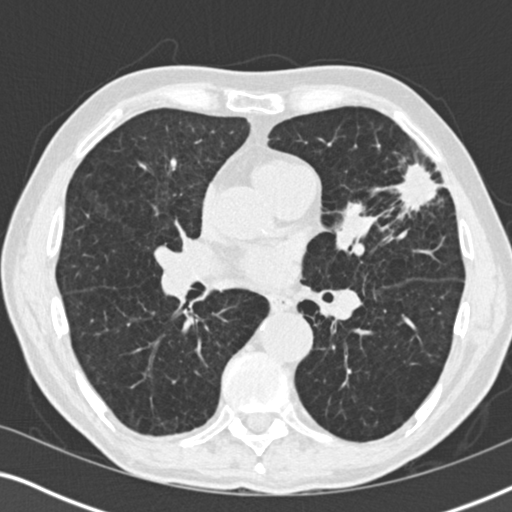
Low-dose screening chest CT, one axial slice; position 99 of 196 along the scan axis; 120 kVp; lung window (W 1500 / L -600 HU); 2 mm slice thickness; 512 × 512 image matrix, field of view 330 × 330 mm.
Outlined on this slice (expert manual segmentation):
- lesion 1 (tumor, upper lobe of left lung): bounding box (x1, y1, x2, y2) in pixels: (396, 163, 439, 208)
- lesion 2 (tumor, upper lobe of left lung): (341, 203, 364, 225)